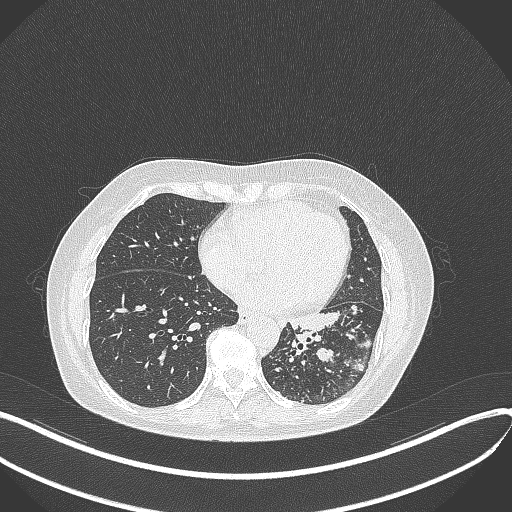
Chest CT, one axial slice; position 152 of 429 along the scan axis; reconstruction kernel B70f; 100 kVp; lung window (W 1500 / L -600 HU); 1 mm slice thickness; 512 × 512 image matrix. Female patient, age 63 years. From the clinical record (not read from this slice): clinical TNM (as recorded): T1b N0 M0.
Outlined on this slice (bounding box drawn by a radiologist):
- lung tumour (recorded histology: adenocarcinoma): bounding box (x1, y1, x2, y2) in pixels: (281, 305, 349, 334)